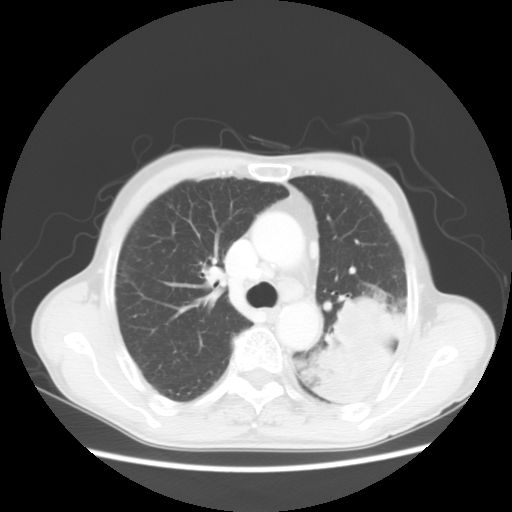
Chest CT, one axial slice; slice 35 of 51 in the series (ordered by position); 120 kVp; lung window (W 1500 / L -600 HU); 5 mm slice thickness; 512 × 512 image matrix, field of view 360 × 360 mm. Patient: male, 64 years. From the clinical record (not read from this slice): clinical TNM (as recorded): T4 N0 M0.
Outlined on this slice (rectangle marked by the reading radiologist):
- lung tumour (recorded histology: squamous cell carcinoma): bounding box <298,286,421,421> (left, top, right, bottom; pixels)